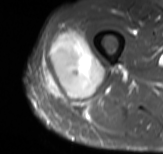
MRI of an extremity soft-tissue mass, one axial slice; position 33 of 61 along the scan axis; STIR; MR volume resampled by the dataset authors to the PET/CT grid (not the native acquisition matrix); 3.27 mm slice thickness; 163 × 154 image matrix. Male patient. From the clinical record (not read from this slice): histological type: poorly differentiated synovial sarcoma; grade: high; site of the primary tumour: right buttock.
Annotated regions visible in this slice (expert contour drawn on MRI and transferred to this co-registered scan by the dataset authors):
- gross tumour volume including surrounding oedema: bounding box <41,28,102,99> (left, top, right, bottom; pixels)
- gross tumour volume (mass): <50,32,102,99>